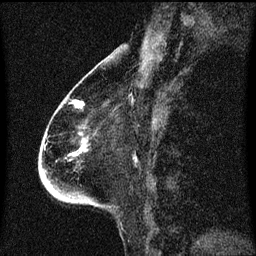
Breast MRI (dynamic contrast-enhanced), one sagittal slice. Position 28 of 60 along the scan axis. Dynamic contrast-enhanced series, image 2 of 3 at this slice position (ordered by acquisition). 1.5 T. TE 4.2 ms, TR 8.4 ms. 2 mm slice thickness. 256 × 256 image matrix, field of view 200 × 200 mm. Patient: female, 68 years. Case-level facts recorded for this patient, not image findings: setting: breast cancer imaged before/during neoadjuvant chemotherapy; receptor status: triple-negative.
Annotated regions visible in this slice (semi-automatically segmented with operator editing):
- analysis volume of interest (the breast-tissue region the enhancement analysis was run in; not a lesion): bounding box <41,96,104,207> (left, top, right, bottom; pixels)
- tumour enhancement mask (voxels above the 70 % enhancement threshold inside the analysis volume of interest): <77,102,86,151>